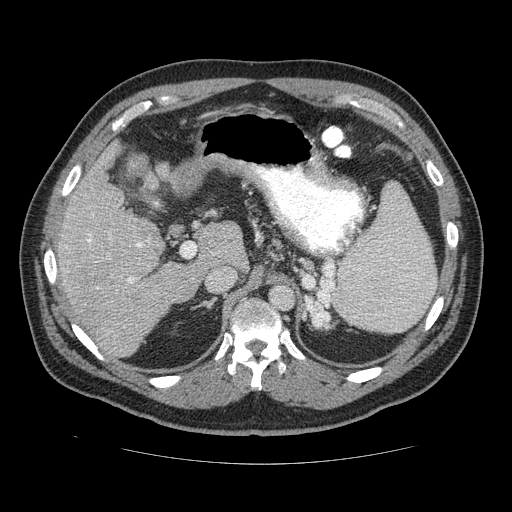
Contrast-enhanced abdominal CT (liver protocol), one axial slice. Slice 82 of 113 in the series (ordered by position). Soft-tissue window (W 400 / L 40 HU). 512 × 512 image matrix. Case-level facts recorded for this patient, not image findings: diagnosis: hepatocellular carcinoma (patient treated with transarterial chemoembolisation; whether this scan precedes or follows treatment is not stated here); TNM stage (as recorded): Stage-II; Child-Pugh class: B; tumour nodularity: multinodular; tumour size: 4.8 cm.
Outlined on this slice (semi-automatic segmentation, software-assisted and operator-edited):
- liver parenchyma outside the tumour (the mass and vessels are separate outlines, so this box may not span the whole liver): bounding box [x1, y1, x2, y2] px = [52, 136, 246, 358]
- liver vessels: [54, 236, 232, 283]